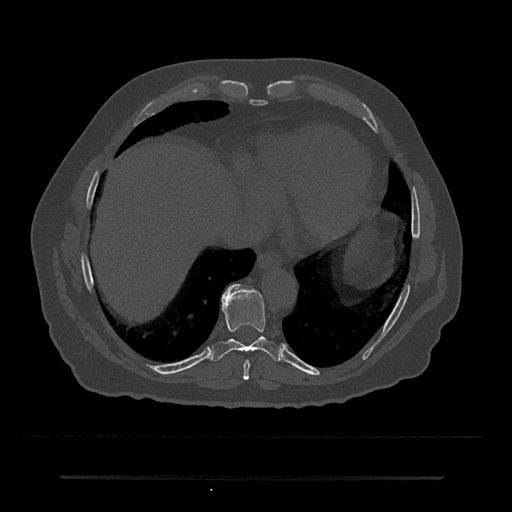
CT including the spine, one axial slice; position 283 of 797 along the scan axis; reconstruction kernel Br40s/3; 120 kVp; bone window (W 1800 / L 400 HU); 512 × 512 image matrix, field of view 437 × 437 mm. Patient: male, 69 years. From the clinical record (not read from this slice): primary cancer: prostate.
Outlined on this slice (semi-automatically segmented with operator editing):
- T8 vertebra: bounding box <243,360,250,380> (left, top, right, bottom; pixels)
- T9 vertebra: <211,284,283,362>